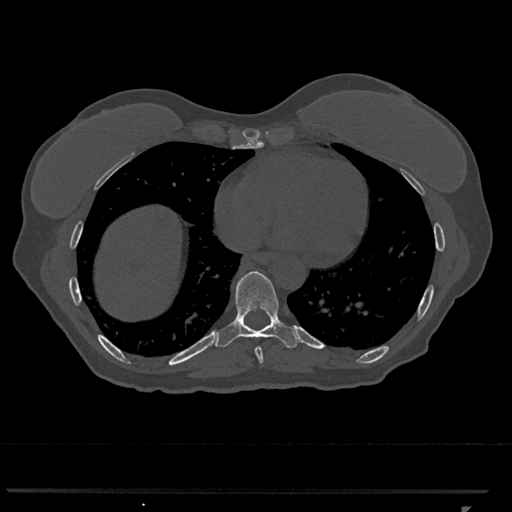
CT including the spine, one axial slice. Position 625 of 793 along the scan axis. Reconstruction kernel Br40s/3. 120 kVp. Bone window (W 1800 / L 400 HU). 0.5 mm slice thickness. 512 × 512 image matrix. Female patient, age 62 years. From the clinical record (not read from this slice): primary cancer: renal.
Annotated regions visible in this slice (semi-automatic segmentation, software-assisted and operator-edited):
- T8 vertebra: bounding box [x1, y1, x2, y2] px = [255, 346, 264, 364]
- T9 vertebra: [215, 271, 299, 348]